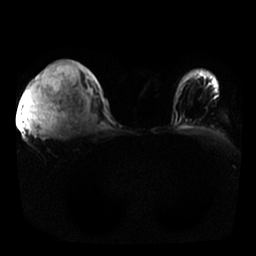
Breast MRI, one axial slice. Position 19 of 25 along the scan axis. Diffusion-weighted series; image 2 of 4 stored at this slice position (different b-values; order by instance number). 1.5 T. 4 mm slice thickness. 256 × 256 image matrix, field of view 350 × 350 mm. Female patient.
Outlined on this slice (expert manual segmentation):
- tumour on diffusion-weighted imaging: box from (x=23, y=63) to (x=62, y=134) px